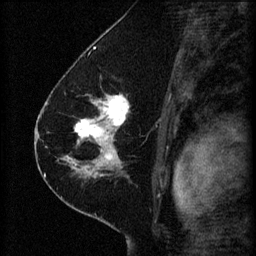
Breast MRI (dynamic contrast-enhanced), one sagittal slice. Slice 37 of 60 in the series (ordered by position). 3 images stored at this slice position (order not interpretable as contrast timing). 1.5 T. TE 4.2 ms, TR 8.2 ms. 2 mm slice thickness. 256 × 256 image matrix, field of view 180 × 180 mm. Patient: female, 41 years.
Outlined on this slice (semi-automatically segmented with operator editing):
- analysis volume of interest (the breast-tissue region the enhancement analysis was run in; not a lesion): bounding box <67,92,165,173> (left, top, right, bottom; pixels)
- tumour enhancement mask (voxels above the 70 % enhancement threshold inside the analysis volume of interest): <67,94,130,173>